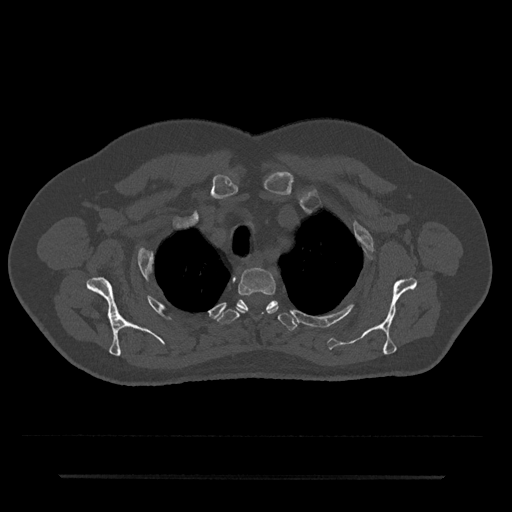
CT including the spine, one axial slice. Position 587 of 797 along the scan axis. Reconstruction kernel Br40s/3. Bone window (W 1800 / L 400 HU). 0.5 mm slice thickness. 512 × 512 image matrix, field of view 437 × 437 mm. Male patient, age 69 years. Case-level facts recorded for this patient, not image findings: primary cancer: prostate.
Annotated regions visible in this slice (semi-automatic segmentation, software-assisted and operator-edited):
- T2 vertebra: bounding box <238,268,278,313> (left, top, right, bottom; pixels)
- T3 vertebra: <217,299,298,331>